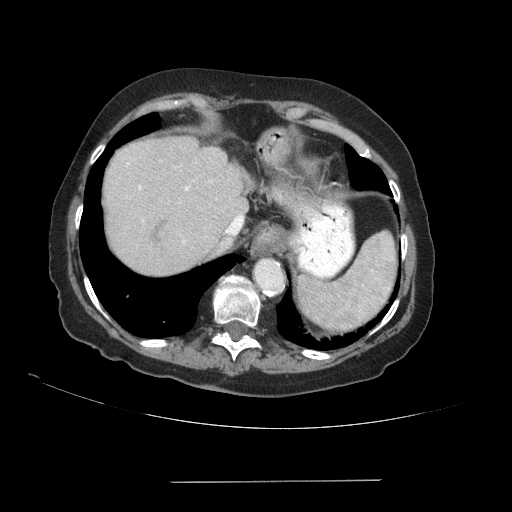
Contrast-enhanced abdominal CT (liver protocol), one axial slice. Slice 74 of 89 in the series (ordered by position). Reconstruction kernel STANDARD. 140 kVp. Soft-tissue window (W 400 / L 40 HU). 512 × 512 image matrix. From the clinical record (not read from this slice): diagnosis: hepatocellular carcinoma (patient treated with transarterial chemoembolisation; whether this scan precedes or follows treatment is not stated here); TNM stage (as recorded): Stage-IVA; Child-Pugh class: A; tumour differentiation: poorly differentiated; tumour nodularity: uninodular.
Annotated regions visible in this slice (semi-automatic segmentation, software-assisted and operator-edited):
- abdominal aorta: bounding box <255,260,282,289> (left, top, right, bottom; pixels)
- liver parenchyma outside the tumour (the mass and vessels are separate outlines, so this box may not span the whole liver): <102,136,248,274>
- liver vessels: <138,186,244,243>